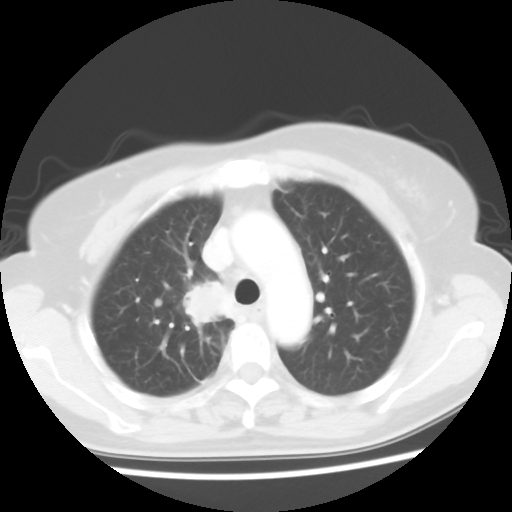
Chest CT, one axial slice. Slice 42 of 56 in the series (ordered by position). Lung window (W 1500 / L -600 HU). 5 mm slice thickness. 512 × 512 image matrix, field of view 314 × 314 mm. Patient: female, 62 years. From the clinical record (not read from this slice): clinical TNM (as recorded): T2 N1 M1a.
Structures marked on this image (rectangle marked by the reading radiologist):
- lung tumour (recorded histology: adenocarcinoma): bounding box <172,272,243,322> (left, top, right, bottom; pixels)